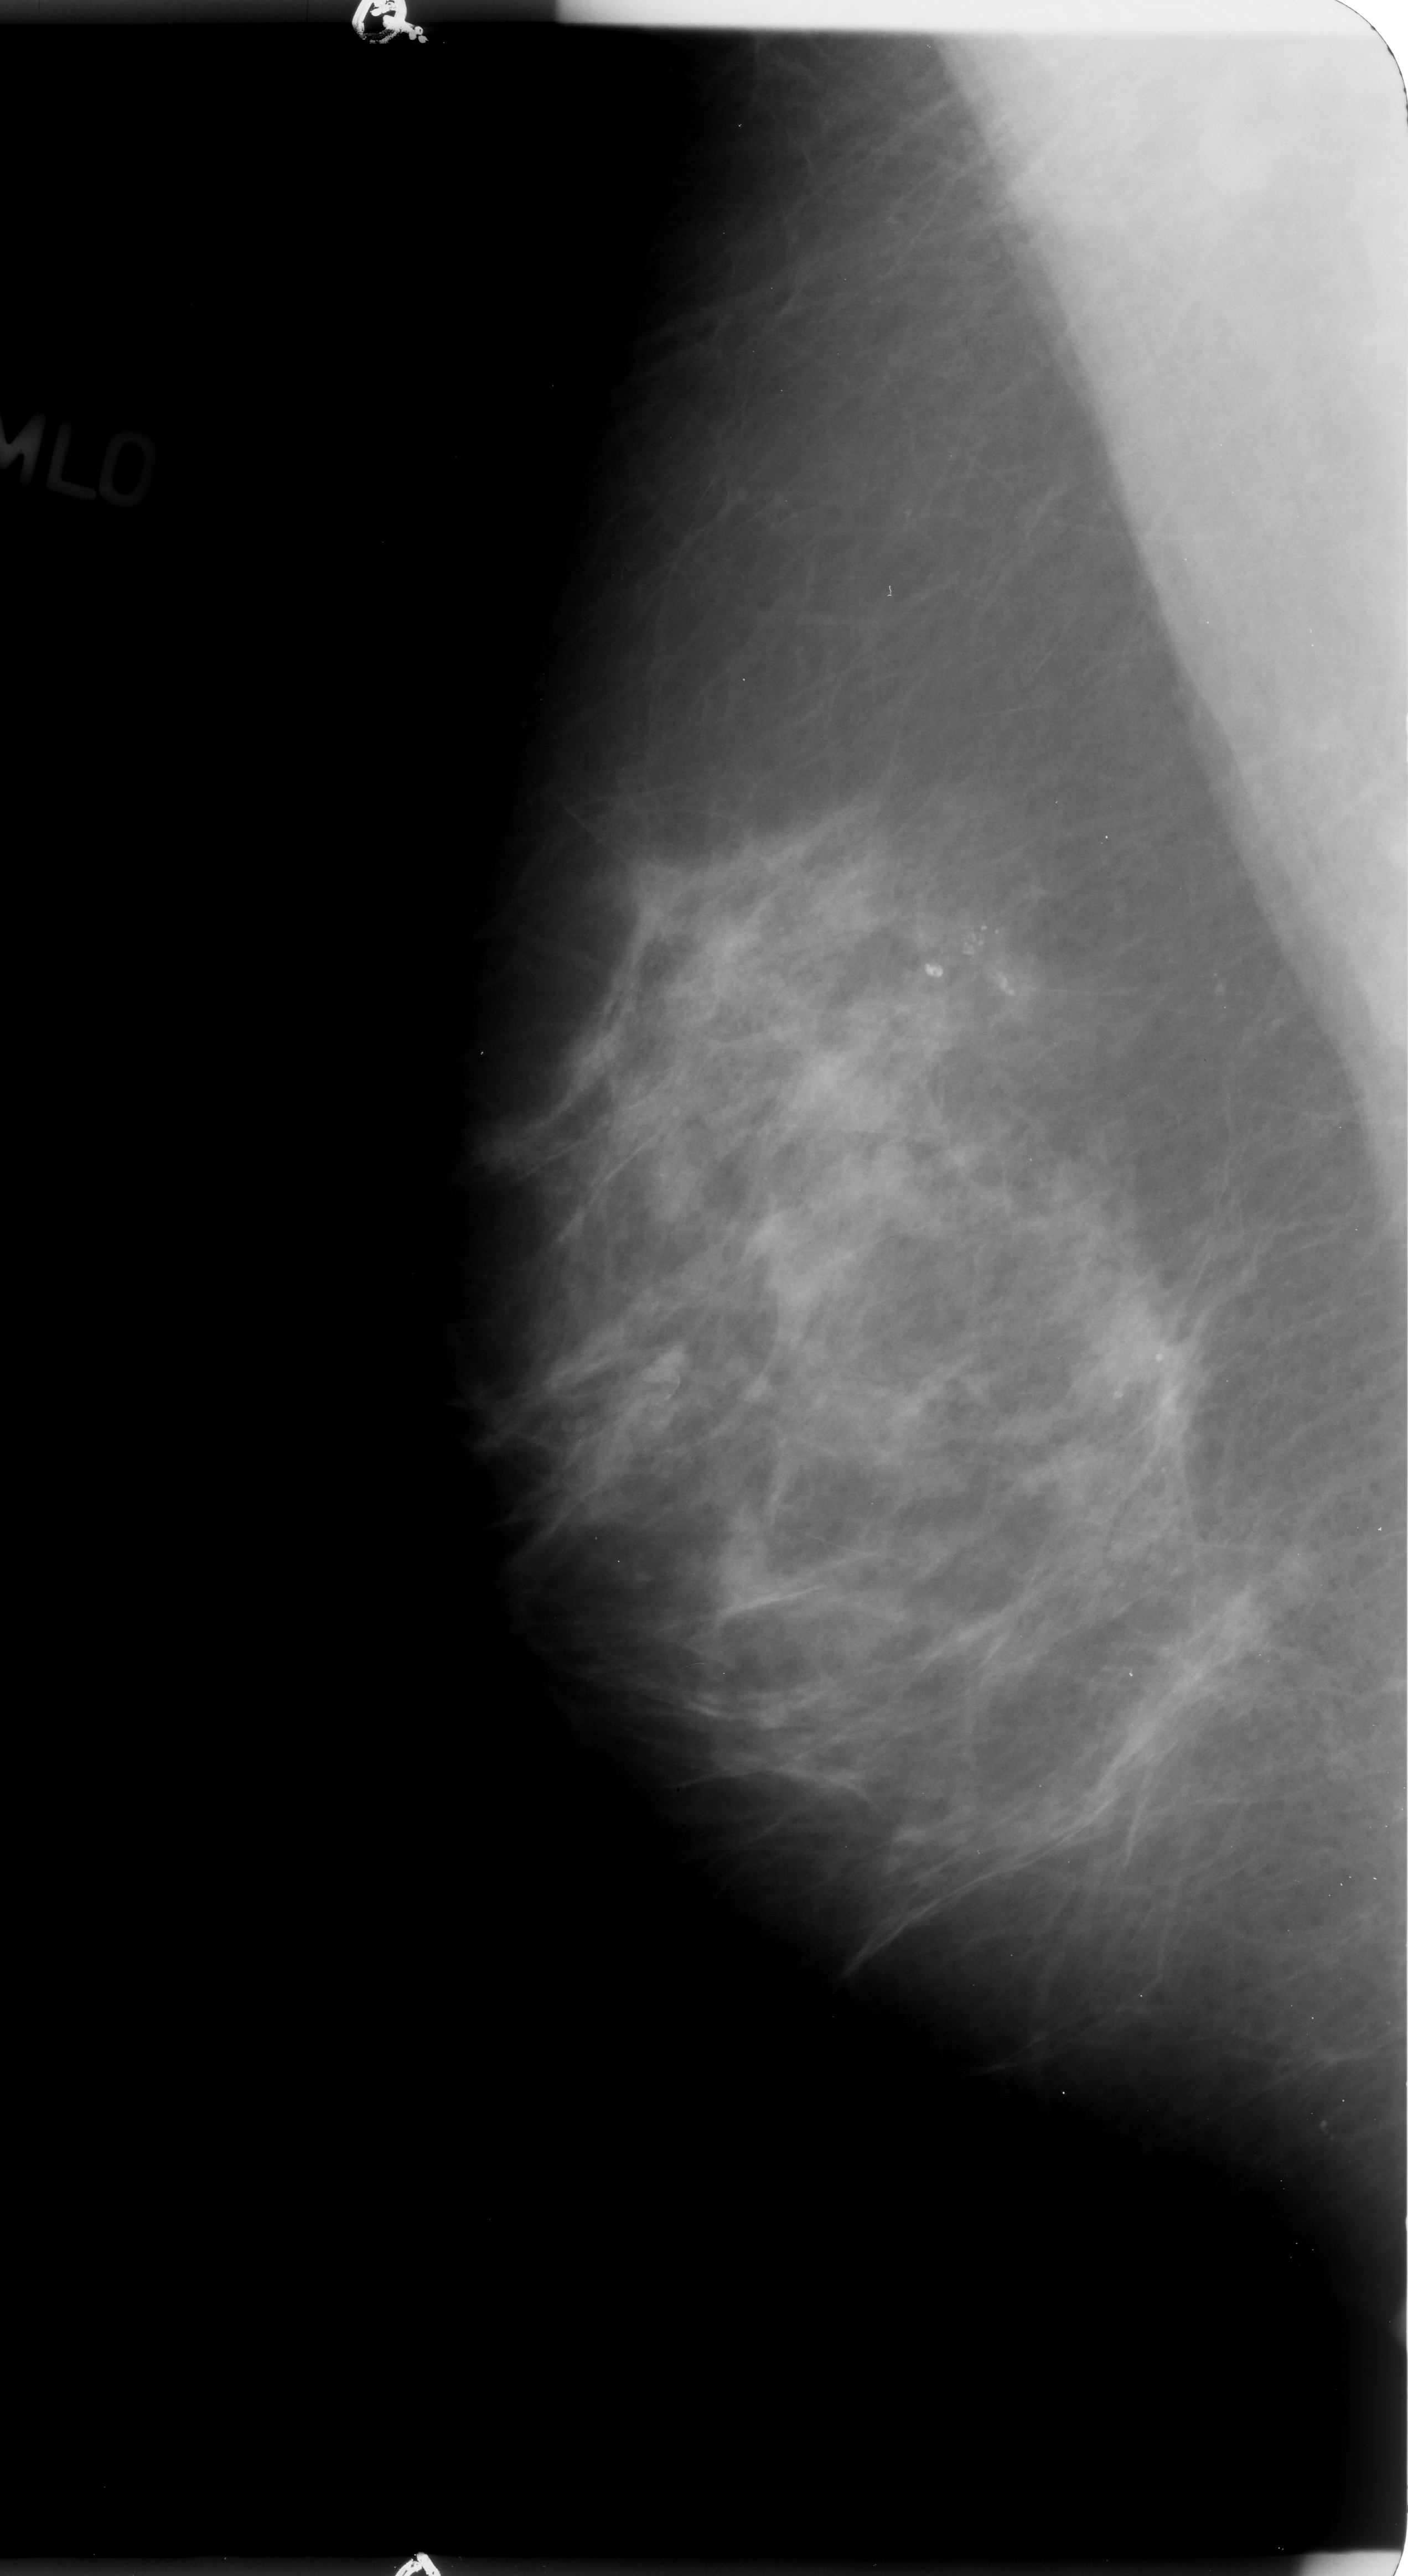
Scanned film-screen mammogram, right breast, mediolateral oblique (MLO) view, breast composition: scattered fibroglandular densities (BI-RADS density category 2 of 4).
Radiologist-marked abnormalities on this image: calcifications, morphology pleomorphic, distribution clustered; BI-RADS assessment category 4; subtlety rating 4 on a 1 (subtle) to 5 (obvious) scale; pathology result (as recorded, not read from the image): benign.